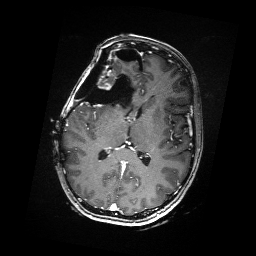
Brain MRI from a brain-tumour surgery series, one axial slice; T1-weighted post-contrast; 256 × 256 image matrix, field of view 256 × 256 mm. Case-level facts recorded for this patient, not image findings: histopathology: Metastatic Carcinoma from Breast primary; tumour location: Right Frontal.
Annotated regions visible in this slice (manually delineated by an expert):
- residual tumour: bounding box [x1, y1, x2, y2] px = [88, 68, 117, 89]